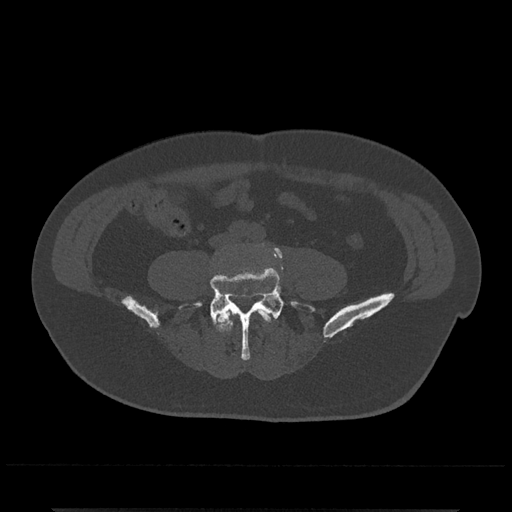
CT including the spine, one axial slice. Slice 105 of 797 in the series (ordered by position). Bone window (W 1800 / L 400 HU). 0.5 mm slice thickness. 512 × 512 image matrix, field of view 393 × 393 mm. Patient: male, 67 years. Case-level facts recorded for this patient, not image findings: primary cancer: prostate.
Structures marked on this image (semi-automatic segmentation, software-assisted and operator-edited):
- L4 vertebra: bounding box <217,309,272,332> (left, top, right, bottom; pixels)
- L5 vertebra: <179,245,315,360>